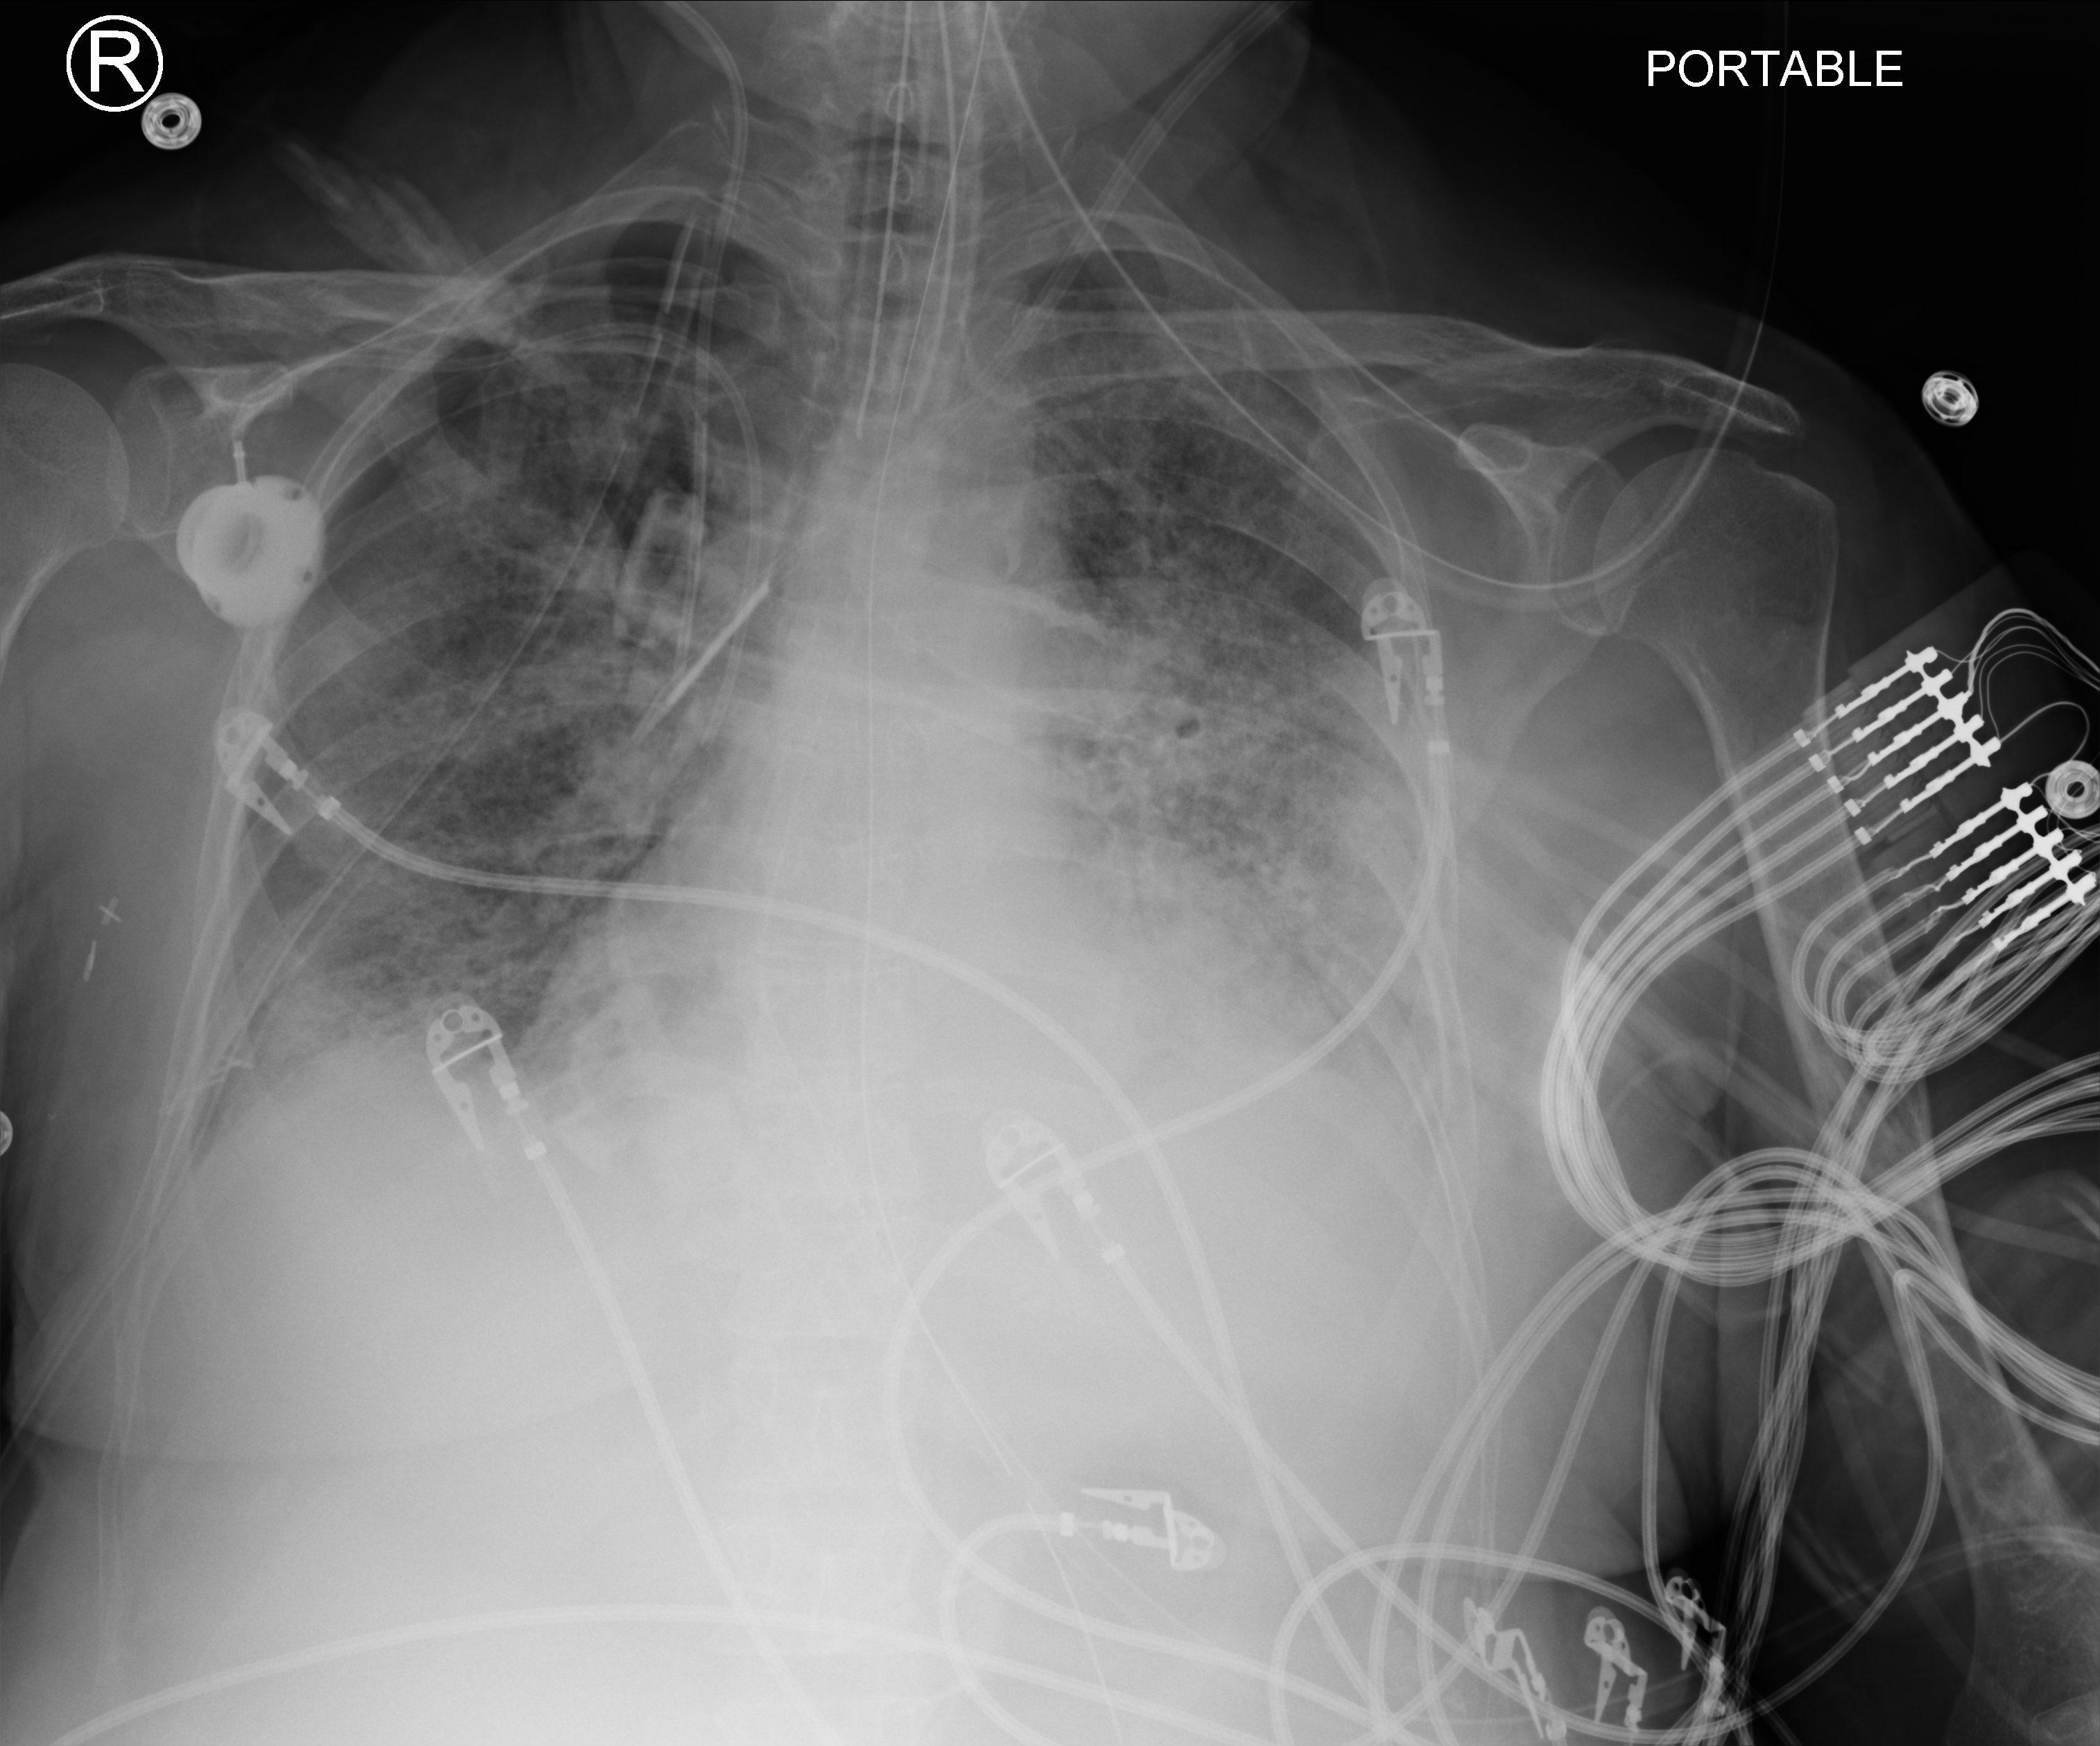
Portable chest radiograph; anteroposterior (AP) projection. Patient hospitalised with COVID-19; female, aged 60–74 years.
Hospital-stay facts (about this admission, not read from this image; timing relative to this image not recorded):
- admitted to intensive care during this hospital stay: yes
- length of hospital stay: 43 days
- smoking status (admission record): former